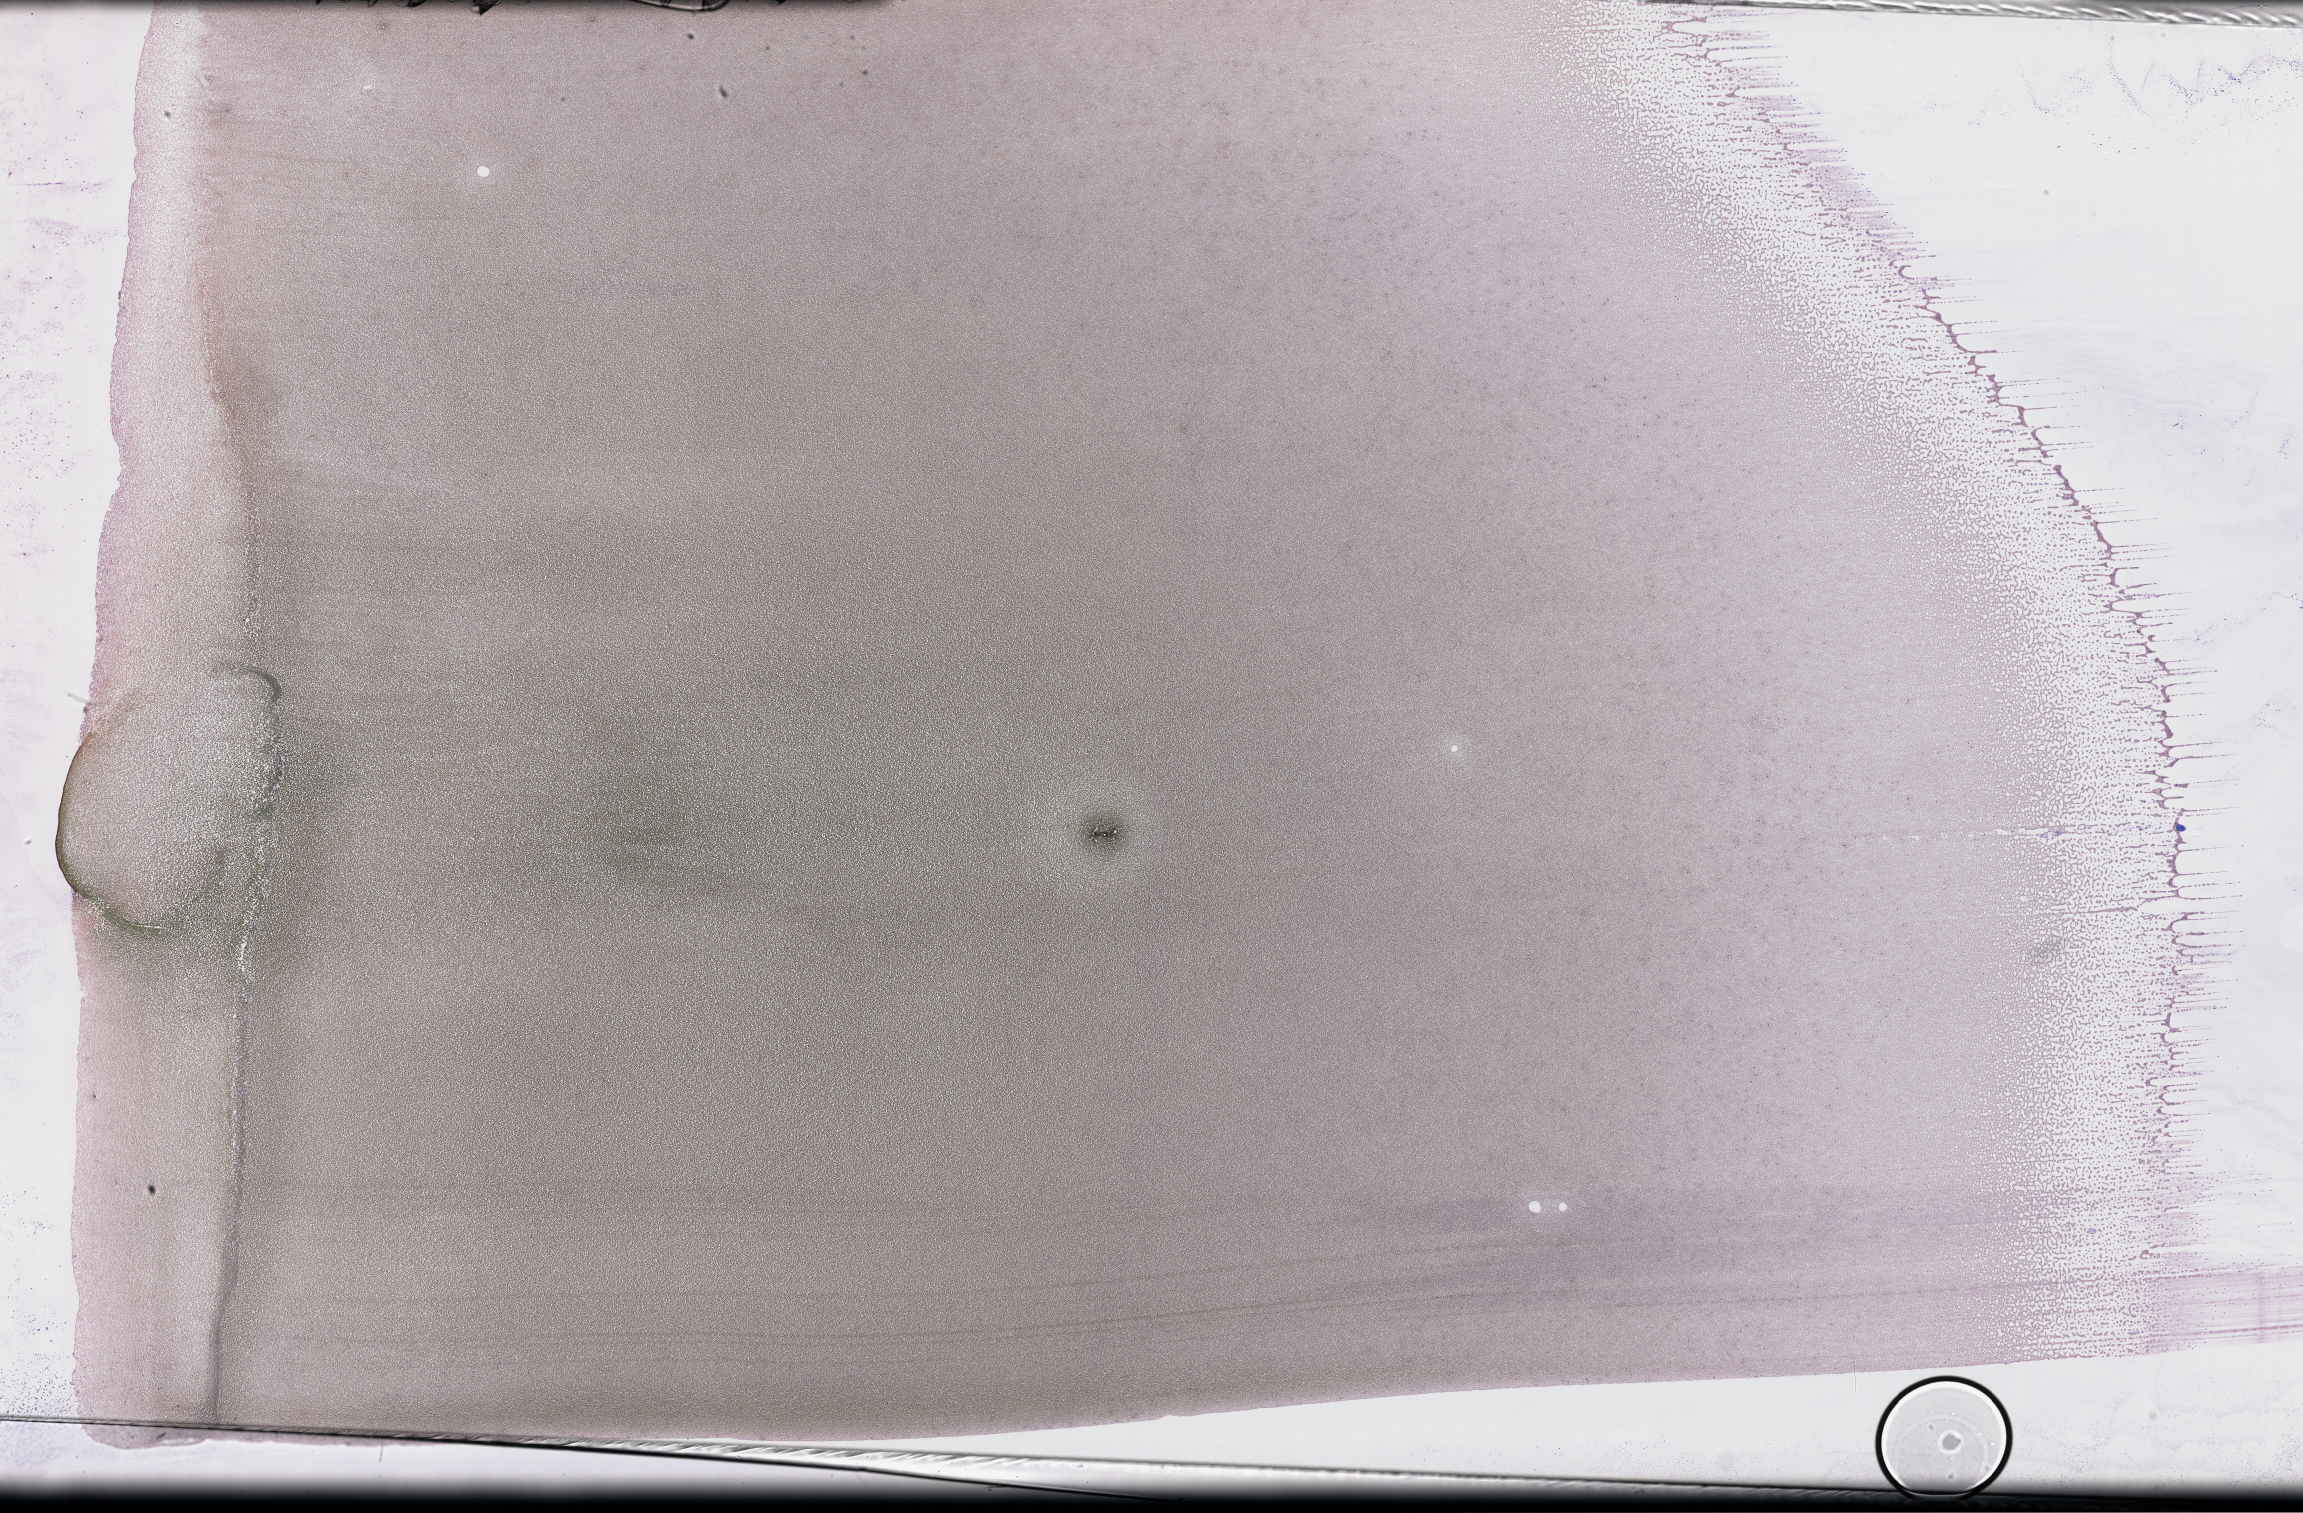
Wright–Giemsa-stained whole blood smear, whole-slide image — shown as a low-resolution overview of the whole scanned area (about 37.2 x 24.4 mm), specimen time point: collected on treatment. Patient sex: female.
• patient diagnosis: Plasma Cell Myeloma